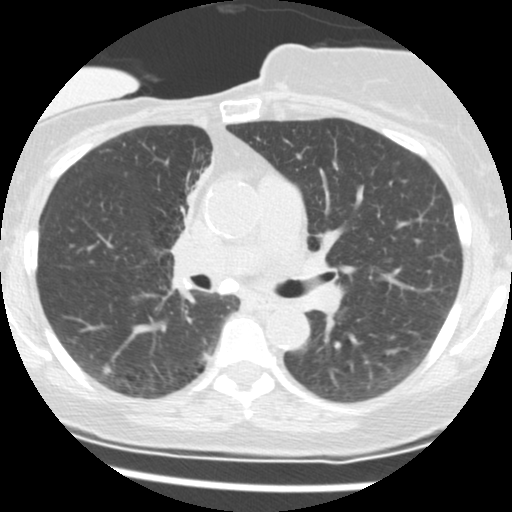
Chest CT (low-dose screening protocol), one axial image; second screening round (one year after baseline); lung window (W 1500 / L -600 HU); 512 × 512 image matrix, field of view 296 × 296 mm. Female participant, aged 56 years at enrolment.
• Expert-annotated lung lesion, bounding box <151,151,206,251> (left, top, right, bottom; pixels).
• The screening reader recorded 2 non-calcified nodules or masses ≥4 mm on this exam (right middle lobe, right lower lobe); which of them this box marks is not recorded.
• Official screen result: positive, change unspecified: nodule(s) >= 4 mm or enlarging nodule(s), mass(es), or other non-specific abnormalities suspicious for lung cancer.
• Participant outcome: lung cancer diagnosed 675 days after this screen (after the third annual screen) — adenocarcinoma, NOS, right upper lobe, stage IIIB (AJCC 6th edition), 8 mm at pathology.